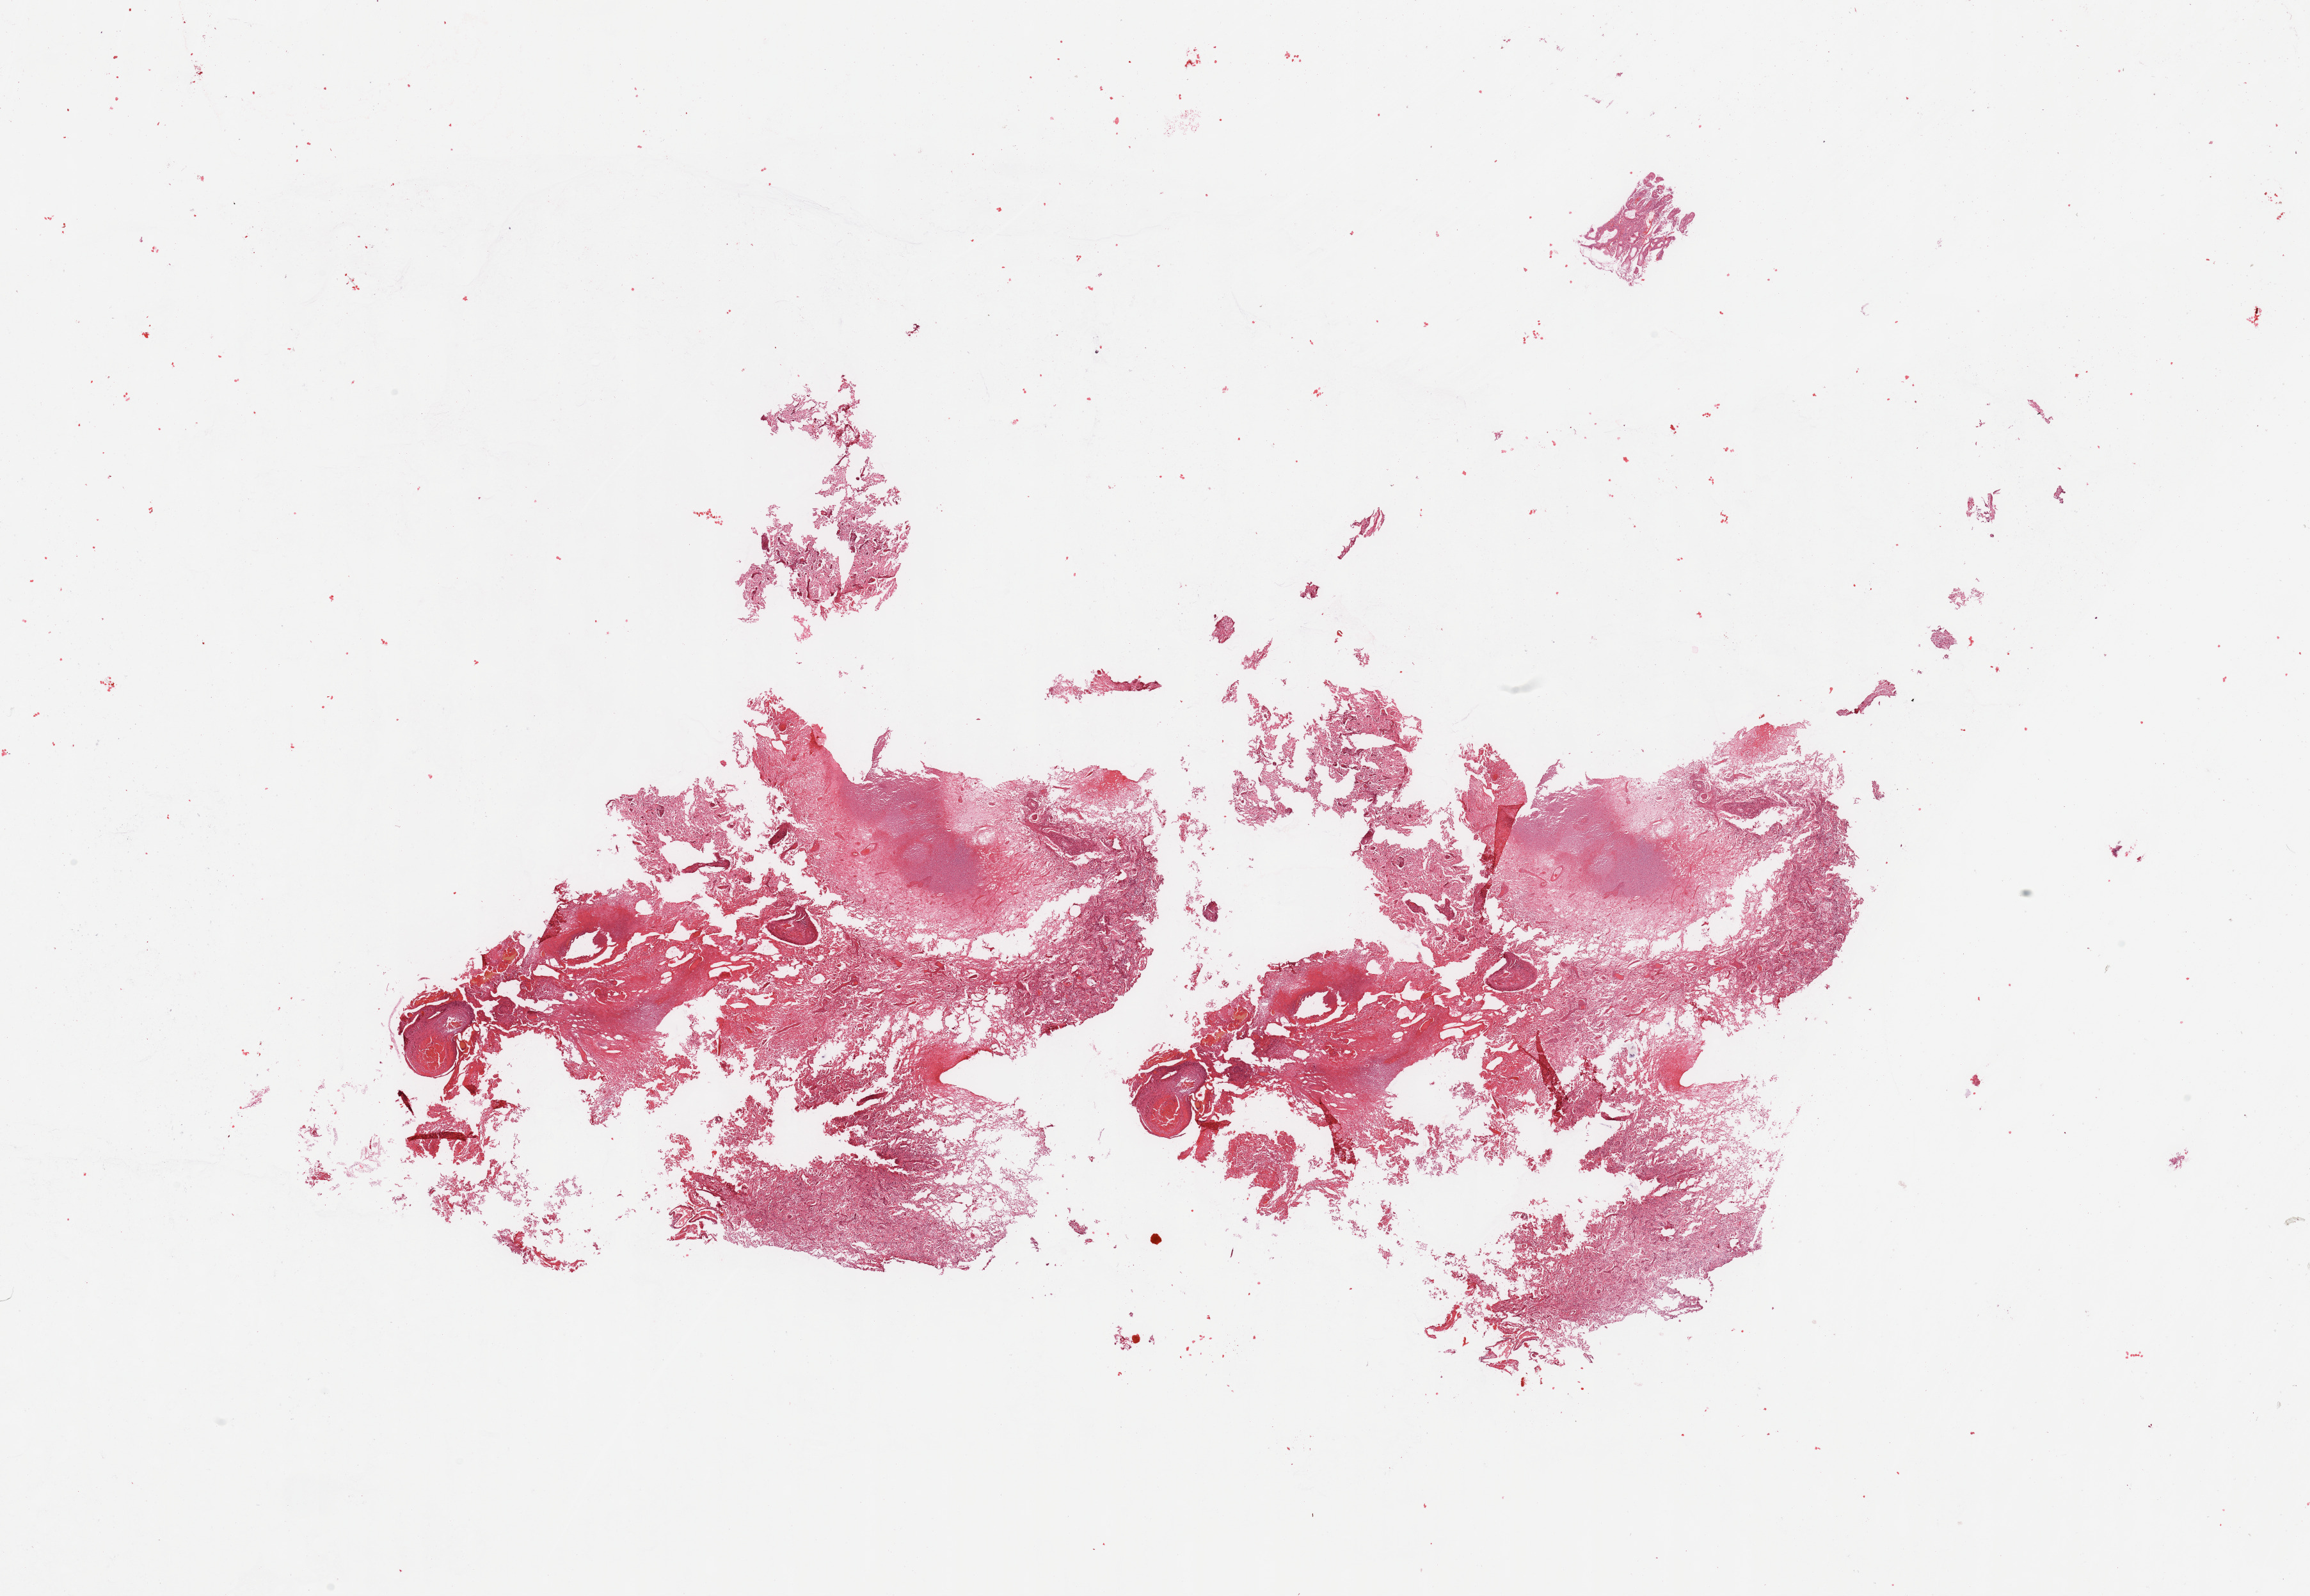
Digitized H&E tissue section (whole slide) — whole scanned area (about 28.5 x 19.7 mm, acquisition: 20x scan) shown as a low-resolution overview; tumour tissue sample, brain. Female, 65 y/o.
Primary tumour site (as recorded): frontal lobe. Histologic diagnosis: Glioblastoma.